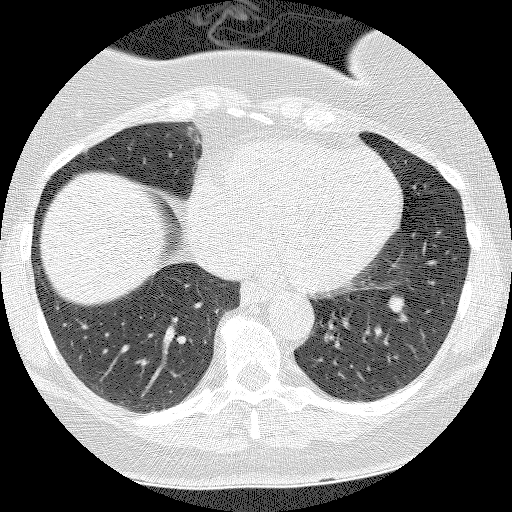
Chest CT (low-dose screening protocol), one axial image. First (baseline) screen. Lung window (W 1500 / L -600 HU). 2.5 mm slice thickness. Slice 93 of 135 in the series. Female participant, aged 55 years at enrolment.
- Lesion marked by an expert reader, bounding box (x1, y1, x2, y2) in pixels: (372, 285, 422, 330).
- The screening reader recorded 3 non-calcified nodules or masses ≥4 mm on this exam (left lower lobe, right lower lobe, right lower lobe); which of them this box marks is not recorded.
- Later outcome: lung cancer diagnosed 1026 days after this screen (after the third annual screen) — carcinoid tumor, NOS, left lower lobe, carcinoid, stage not assessed, 10 mm at pathology.